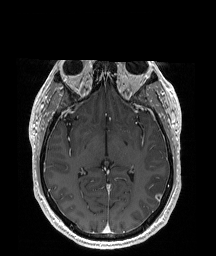
Brain MRI from a brain-tumour surgery series, one axial slice. Position 107 of 192 along the scan axis. T1-weighted post-contrast. 216 × 256 image matrix, field of view 219 × 260 mm. From the clinical record (not read from this slice): histopathology: Glioblastoma; WHO grade: 4; IDH mutation: no.
Outlined on this slice (expert manual segmentation):
- tumour: bounding box <145,174,166,201> (left, top, right, bottom; pixels)